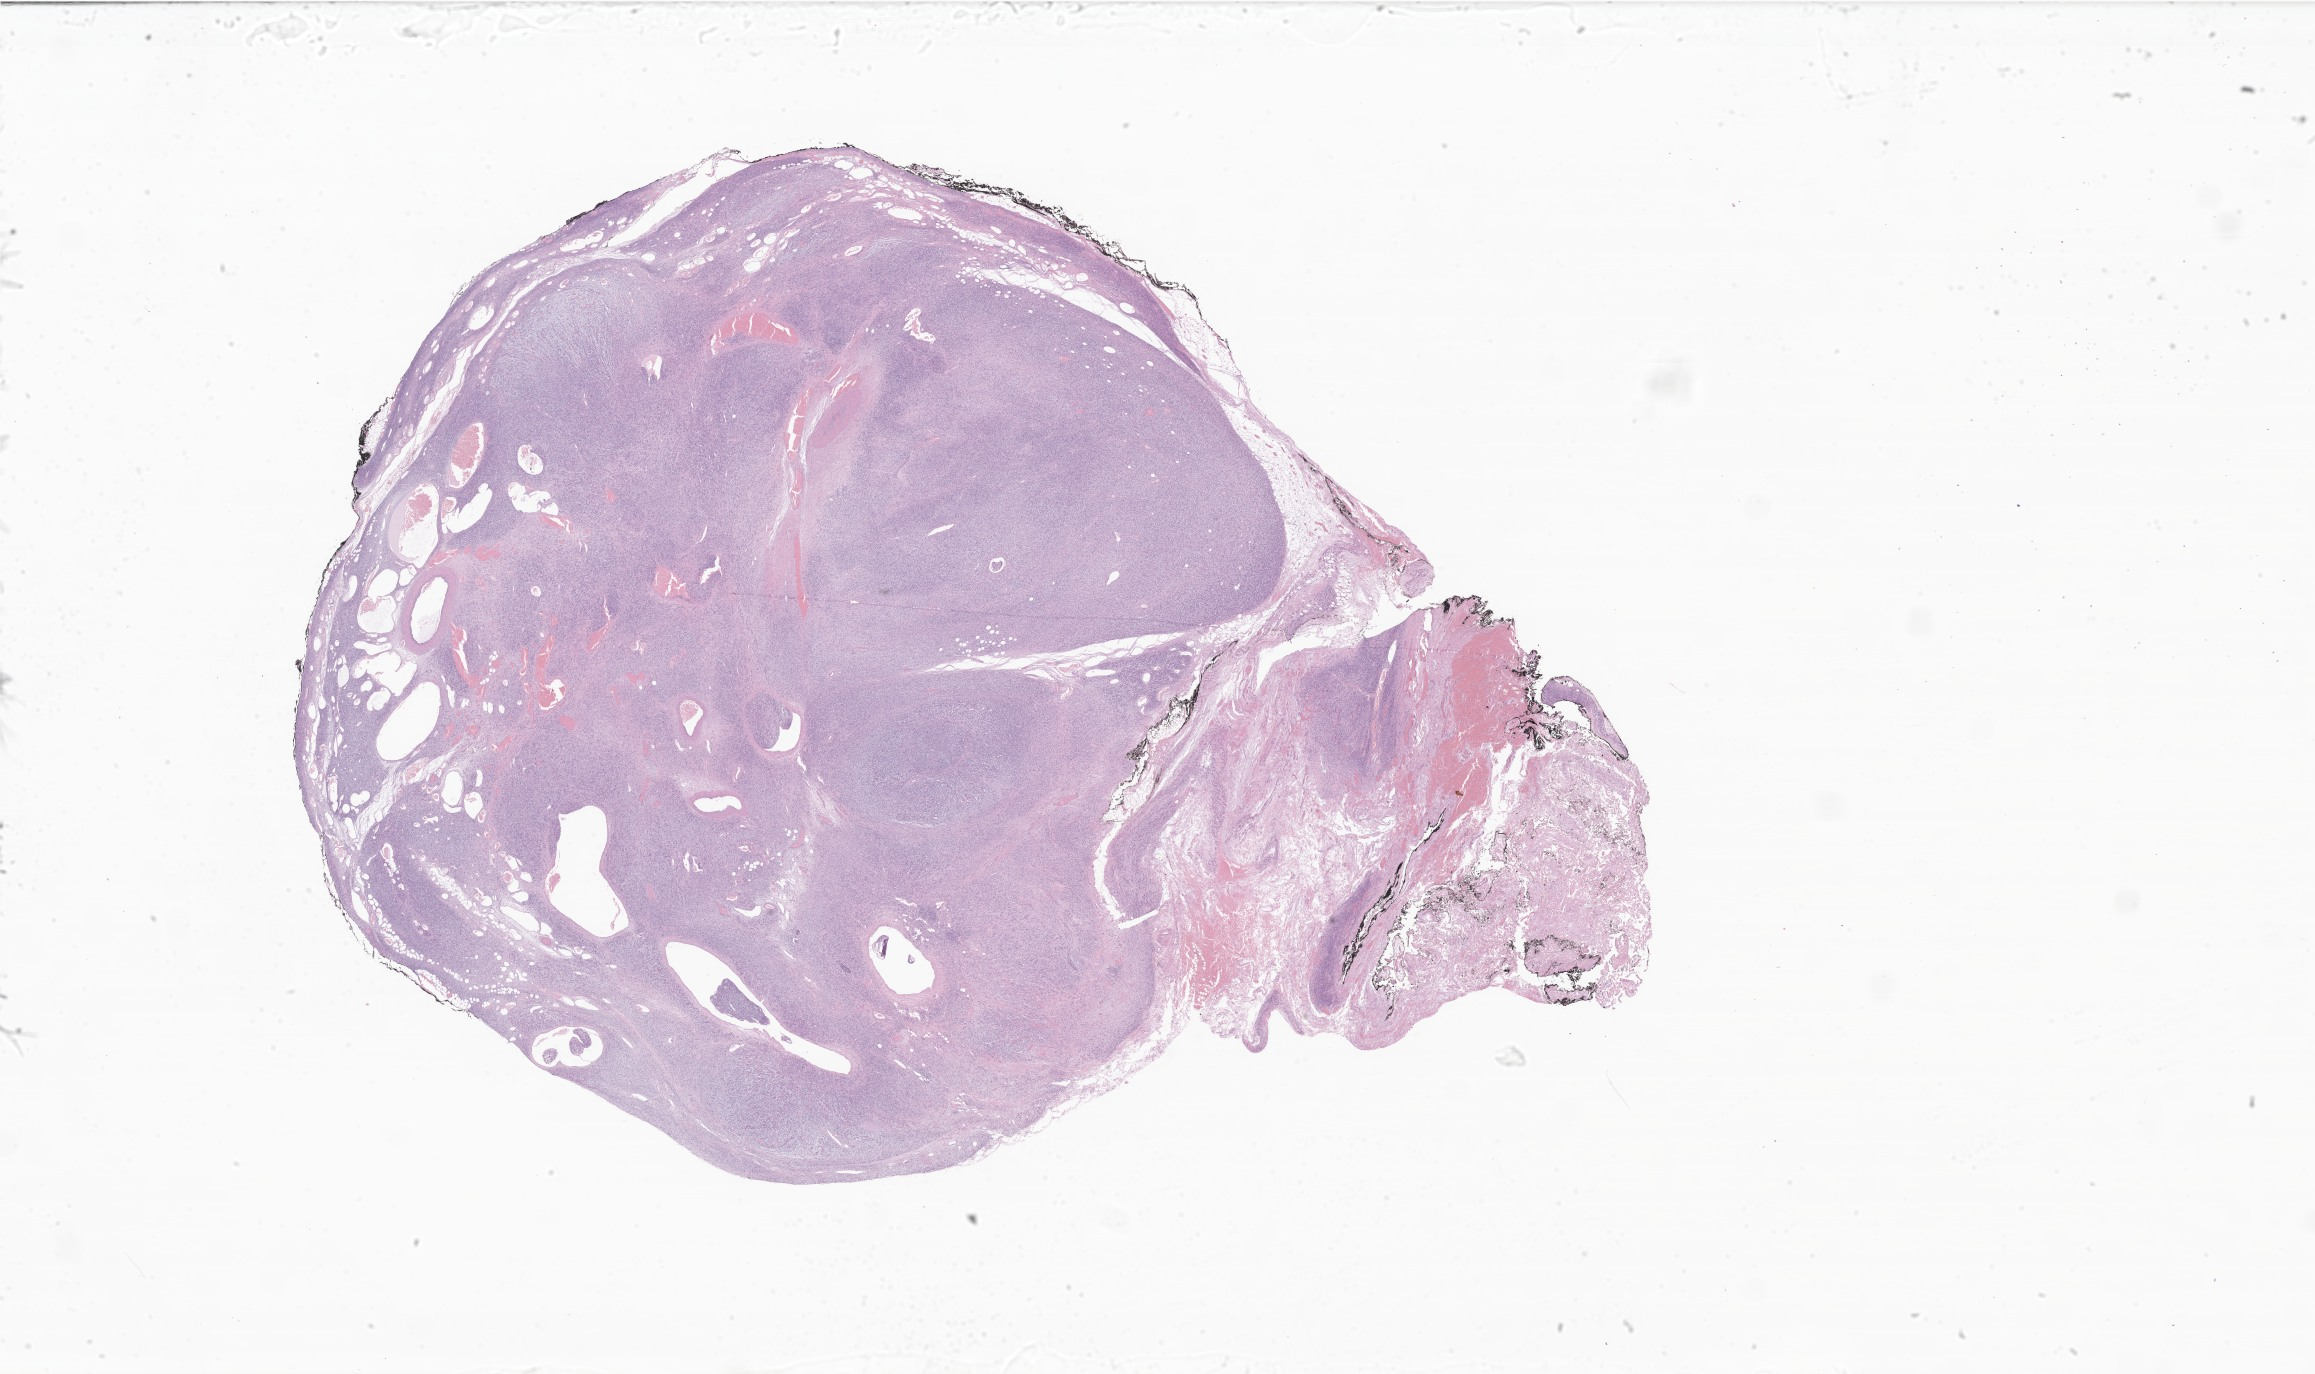
Hematoxylin and eosin (H&E) whole-slide image of tumor tissue from the testis, low-resolution overview of the scanned area, about 39.0 x 23.2 mm; FFPE section. Patient male; age 190 months.
Diagnosis (ICD-O-3 morphology term): Embryonal rhabdomyosarcoma, NOS.